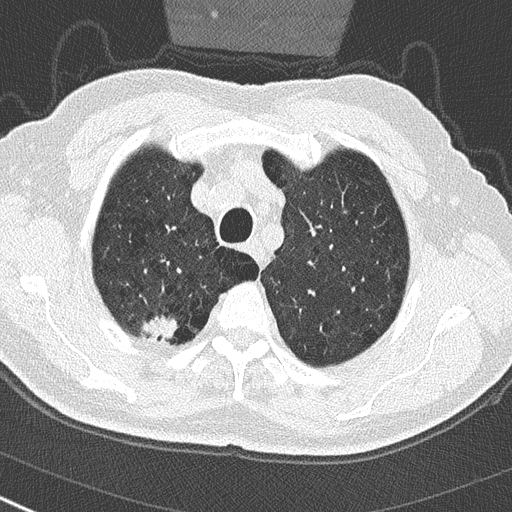
Low-dose screening chest CT, axial slice. First (baseline) screen. Lung window (W 1500 / L -600 HU). 2 mm slice thickness. Lung (sharp) reconstruction kernel (B50f). 120 kVp. 512 × 512 image matrix. Male participant, aged 65 years at enrolment.
Lesion marked by an expert reader, box from (x=136, y=304) to (x=183, y=351) px. Reader record for this screening exam (exam-level; its link to the box is not recorded): non-calcified nodule or mass ≥4 mm, right upper lobe, 24 × 19 mm, spiculated (stellate) margins, soft tissue attenuation. Official screen result: positive, change unspecified: nodule(s) >= 4 mm or enlarging nodule(s), mass(es), or other non-specific abnormalities suspicious for lung cancer. Lung cancer was diagnosed 32 days after this screen: non-small cell carcinoma, right upper lobe, poorly differentiated (G3), stage IA (AJCC 6th edition), 29 mm at pathology.